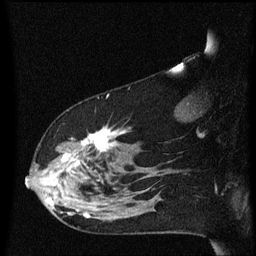
Breast MRI (dynamic contrast-enhanced), one sagittal slice; slice 43 of 60 in the series (ordered by position); dynamic contrast-enhanced series, image 2 of 3 at this slice position (ordered by acquisition); 1.5 T; TE 4.2 ms, TR 8.4 ms; 256 × 256 image matrix, field of view 200 × 200 mm. Female patient, age 48 years.
Outlined on this slice (semi-automatic segmentation, software-assisted and operator-edited):
- analysis volume of interest (the breast-tissue region the enhancement analysis was run in; not a lesion): bounding box [x1, y1, x2, y2] px = [31, 128, 134, 225]
- tumour enhancement mask (voxels above the 70 % enhancement threshold inside the analysis volume of interest): [62, 130, 125, 219]